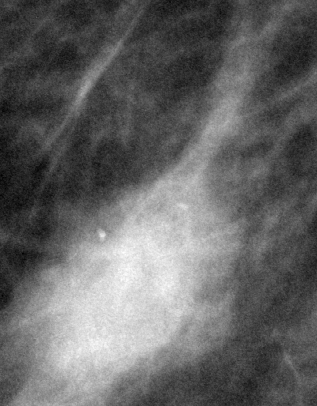
Cropped region of a digitized screen-film mammogram centred on a radiologist-marked abnormality; right breast; MLO view; BI-RADS breast density category 1 (scale 1–4).
Marked abnormality: mass, shape oval, margins microlobulated; BI-RADS assessment category 4; pathology (as recorded): malignant.